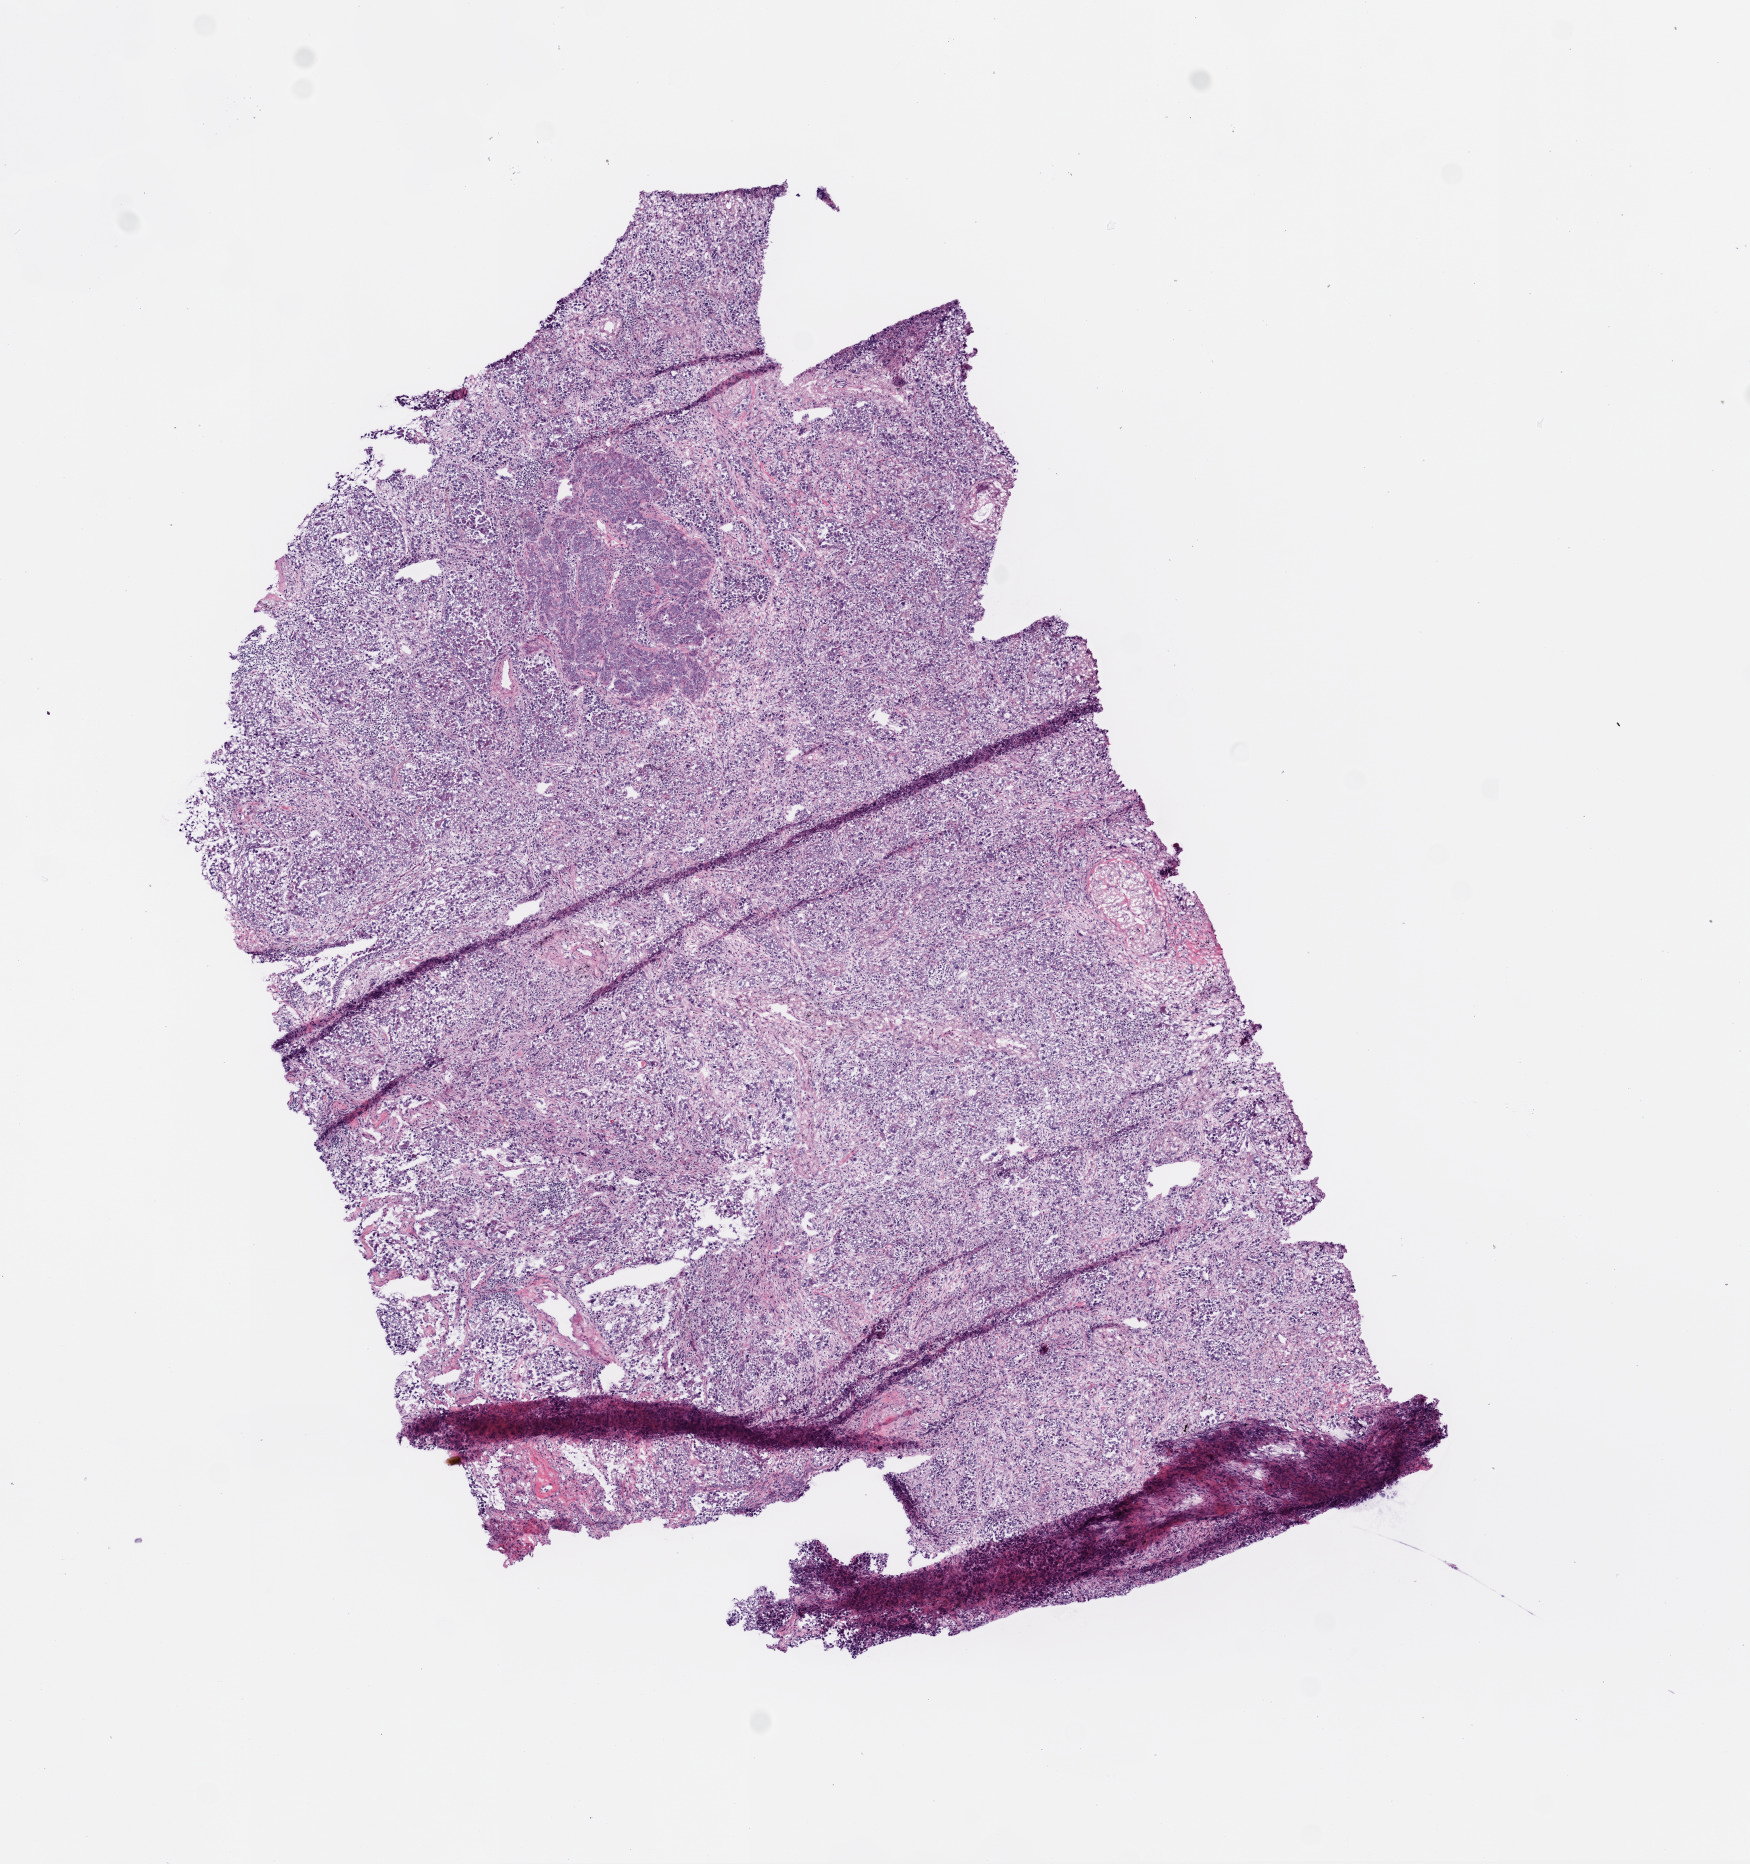
Digitized H&E tissue section (whole slide), shown as a low-resolution overview of the whole scanned area (about 7.0 x 7.5 mm, from a 20x scan). Frozen section from the bottom of the tissue portion. Primary tumour sample from the lung. Female, age 65 years at initial diagnosis. Slide review estimates, as recorded: tumour cells 90%, tumour nuclei 80%, normal cells 0%, stromal cells 10%, necrosis 0%. Infiltration values recorded for this section: lymphocyte infiltration 8%.
- histologic diagnosis: Adenocarcinoma, NOS (lower lobe, lung)
- AJCC pathologic stage: IIB